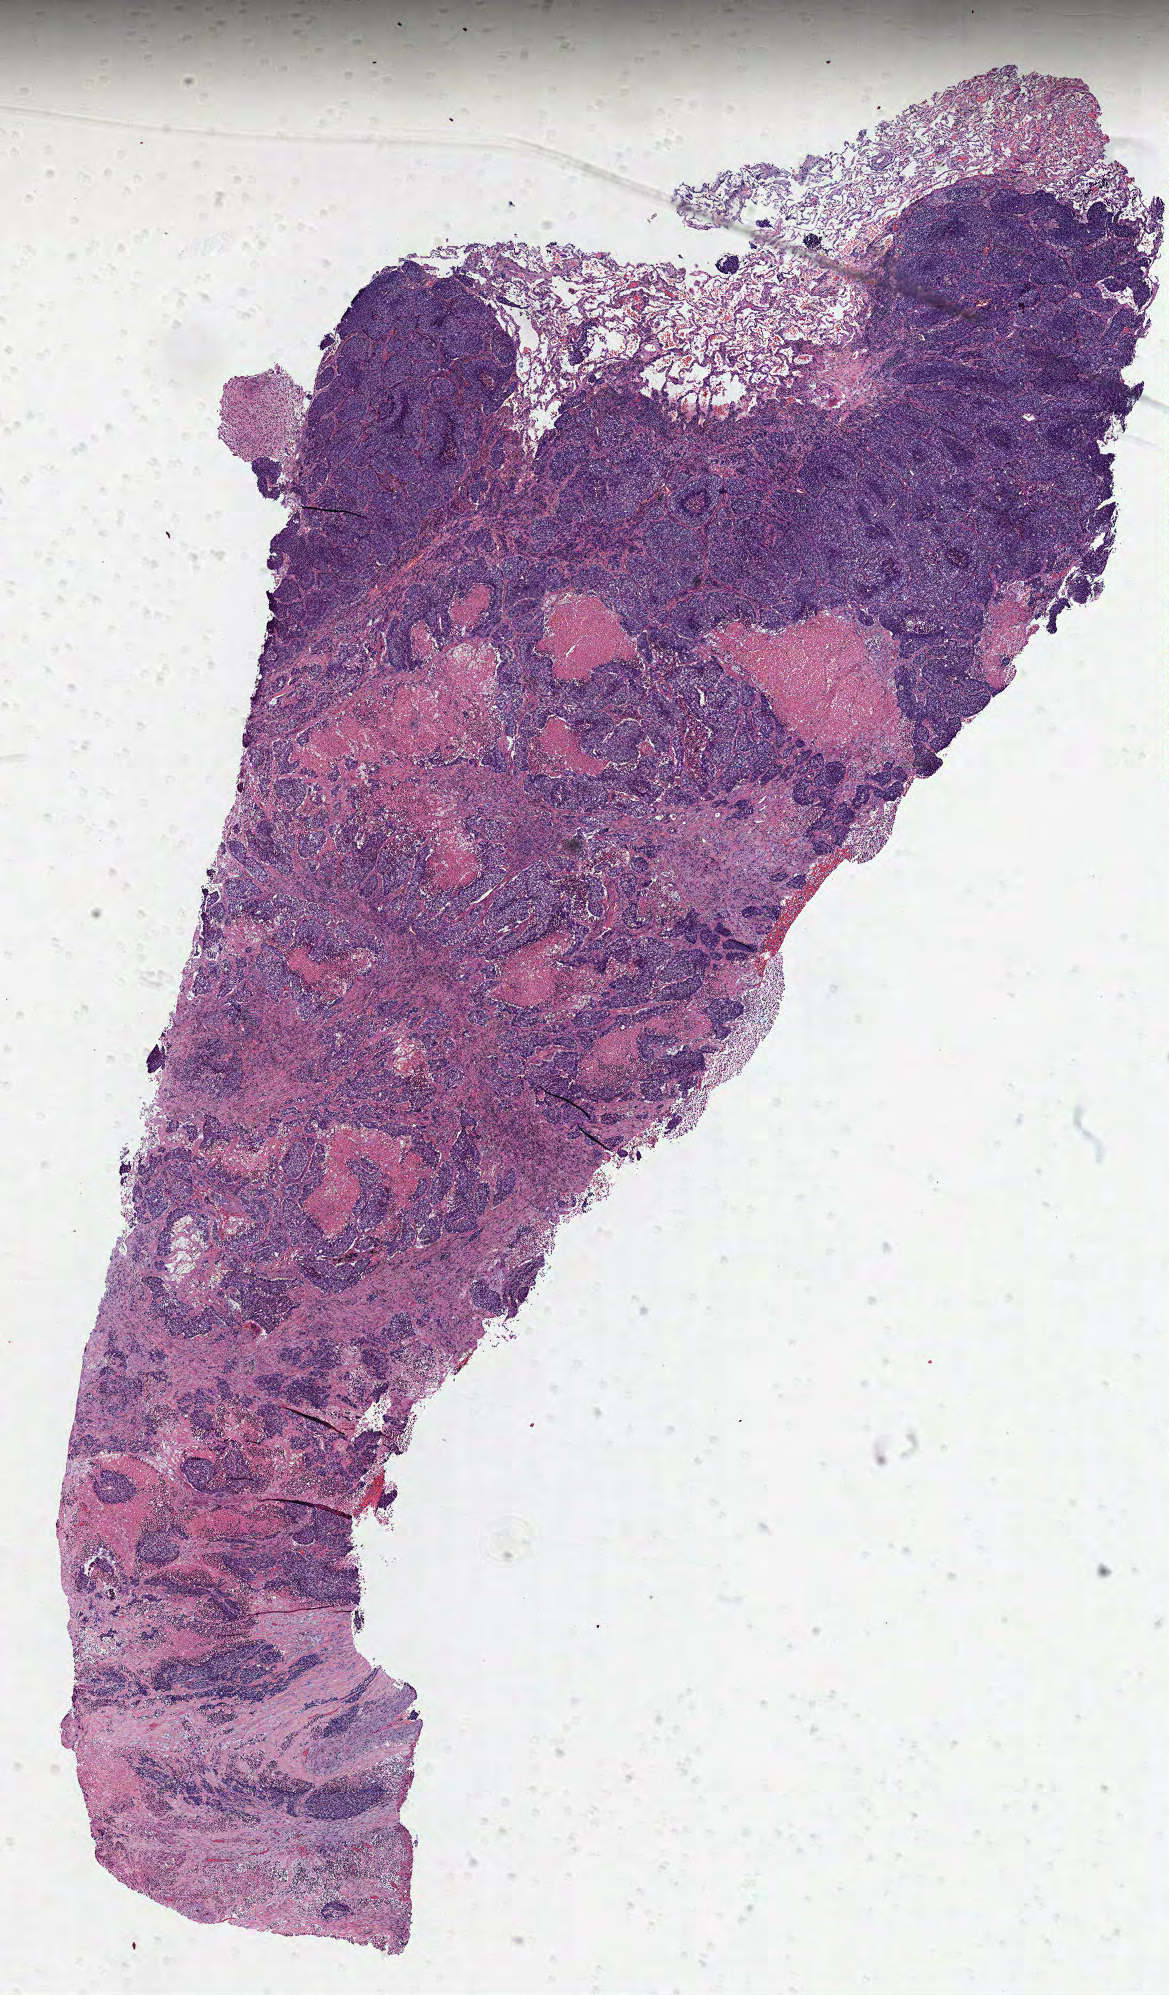
Whole-slide histology image, H&E-stained — shown as a low-resolution overview of the whole scanned area (about 9.4 x 16.1 mm, slide scanned at 40x). Formalin-fixed paraffin-embedded (FFPE) diagnostic section. Primary tumour sample from the lung. Patient: male, age at initial diagnosis 59 years.
Histologic diagnosis: Adenocarcinoma, NOS (upper lobe, lung).